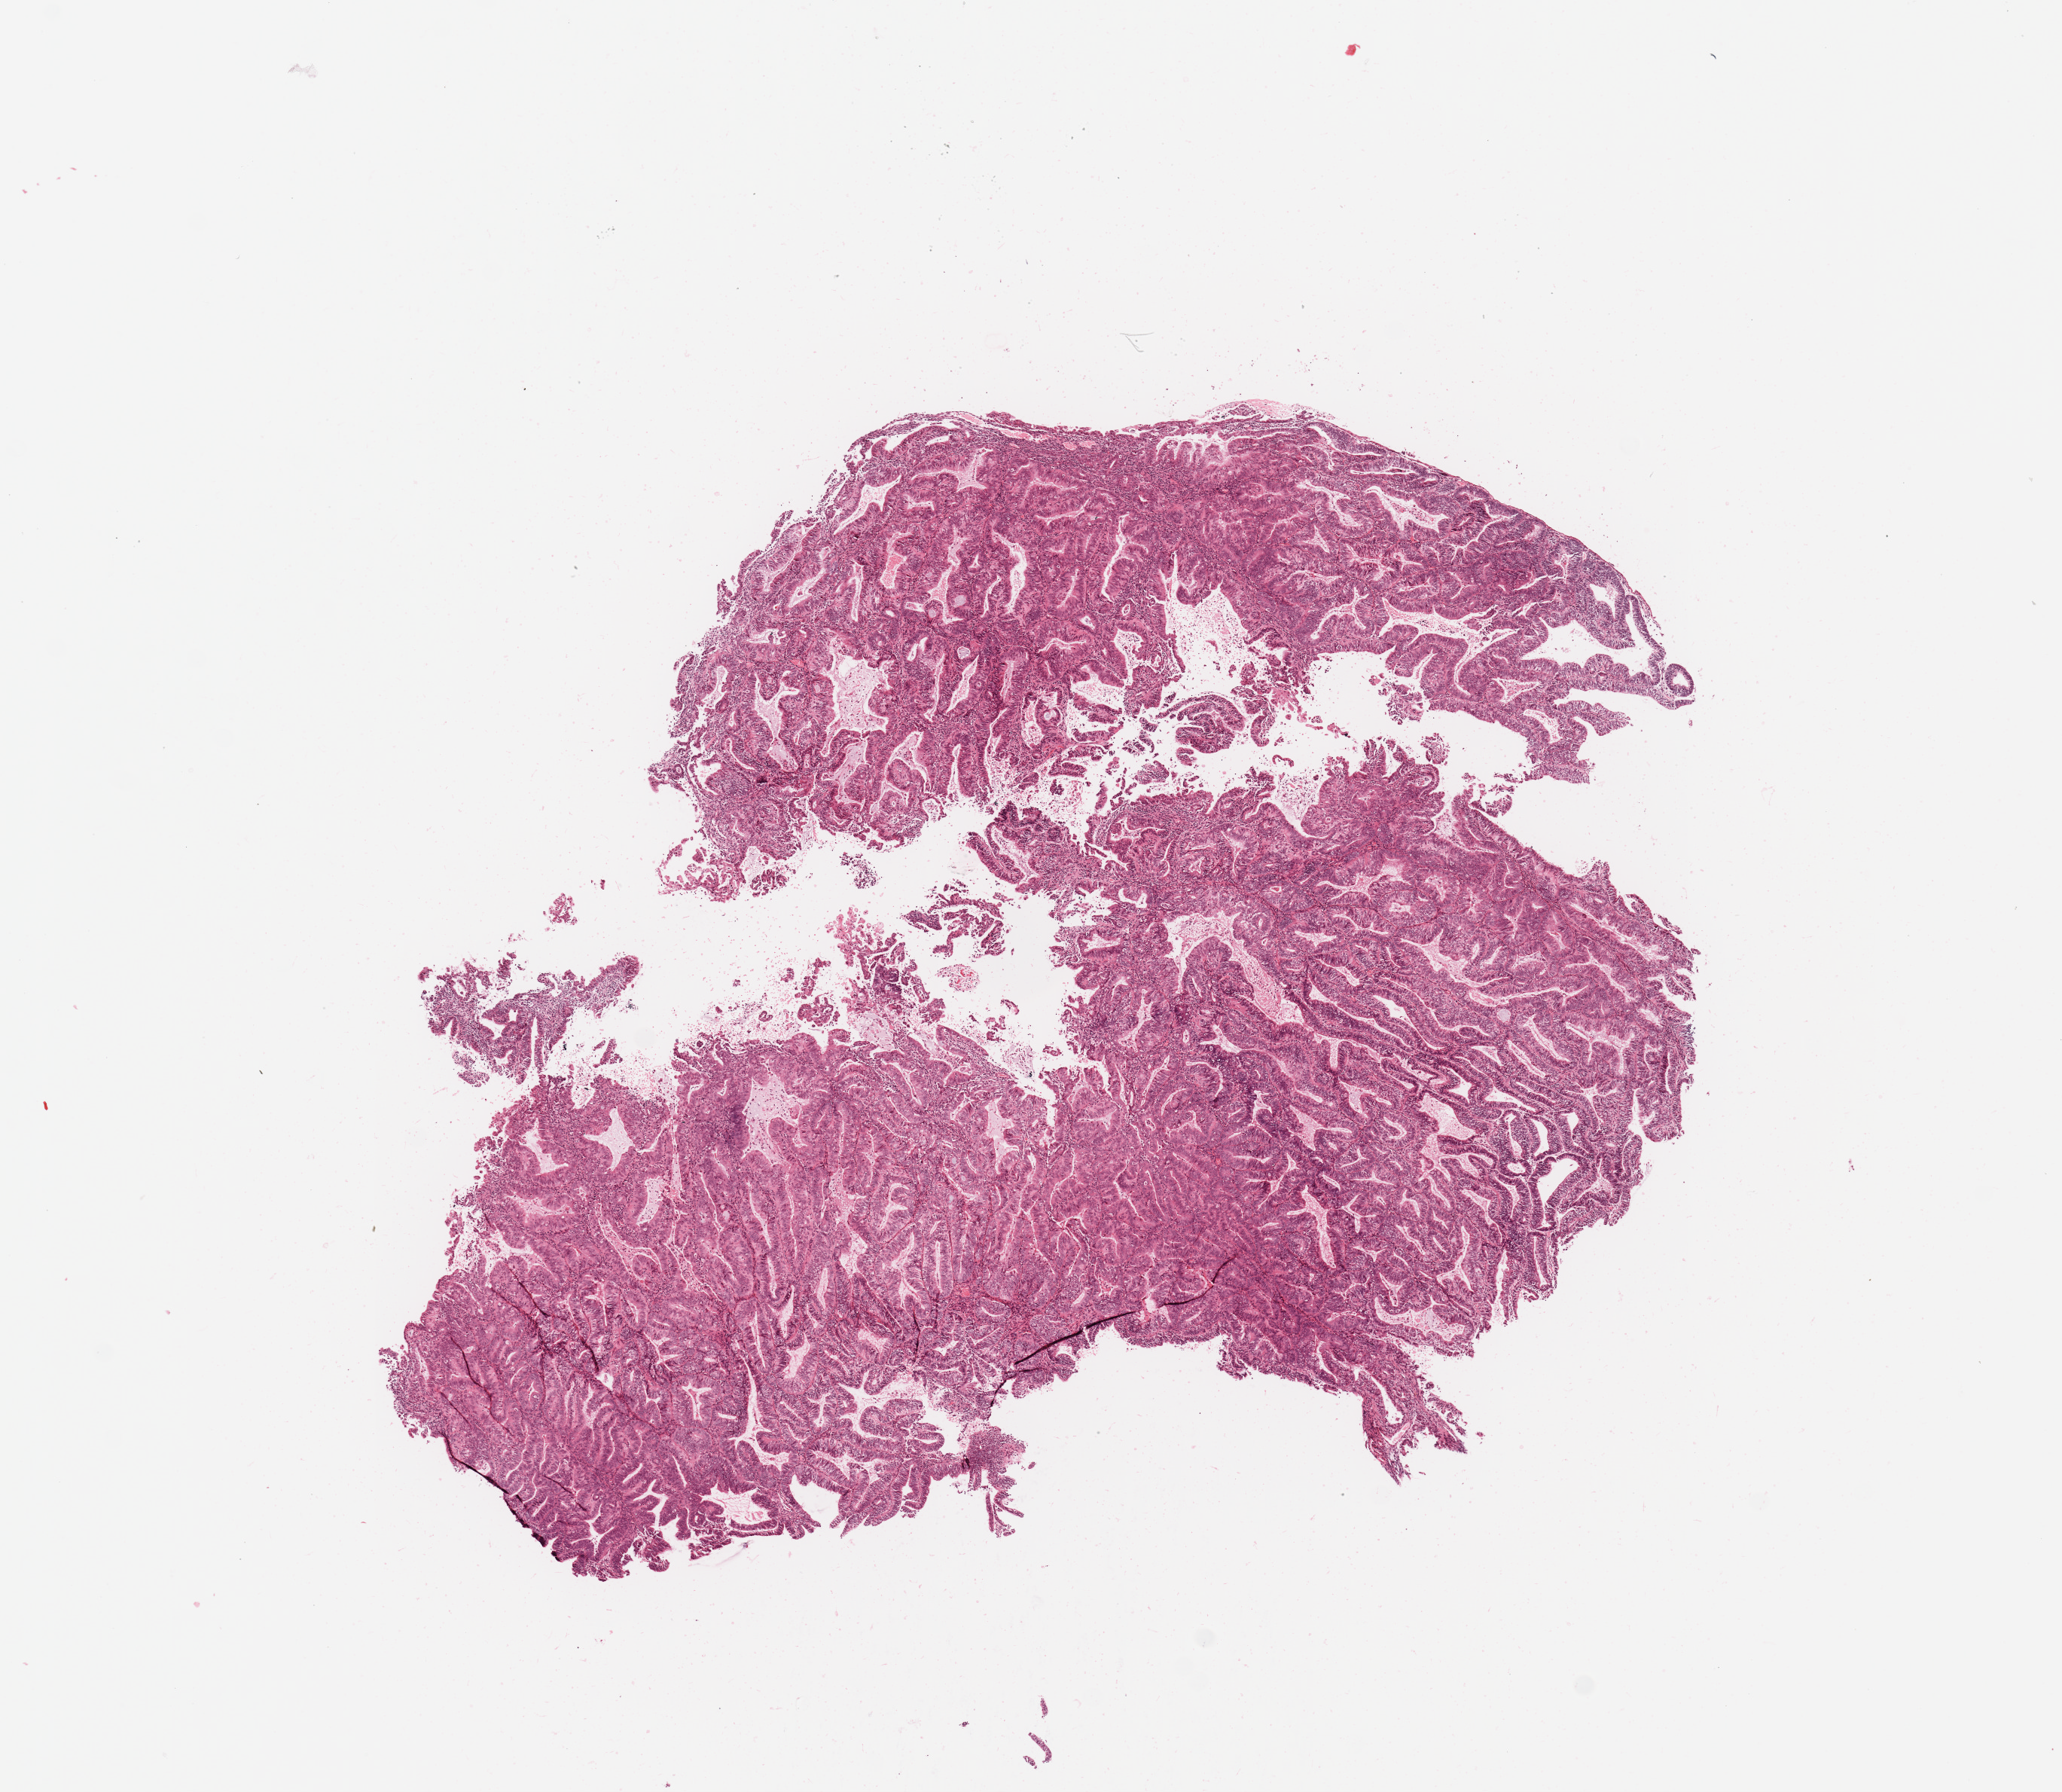
H&E whole-slide image, low-resolution overview of the scanned area, about 10.8 x 9.4 mm (slide scanned at 20x), tumour tissue sample, sampled site: uterus. 59-year-old female patient. Histologic grade: G1 (well differentiated). Composition of this section per pathologist review: tumour nuclei 90%, necrosis 0%.
Histologic diagnosis: Endometrioid adenocarcinoma, NOS. AJCC pathologic stage: IA.